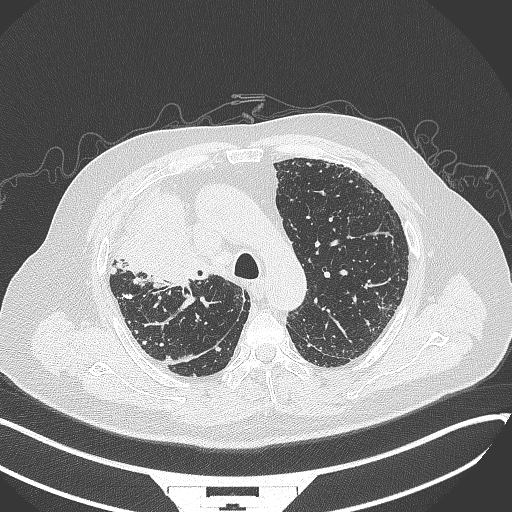
Chest CT, one axial slice. Position 255 of 384 along the scan axis. Lung window (W 1500 / L -600 HU). 1 mm slice thickness. 512 × 512 image matrix, field of view 400 × 400 mm. Patient: male, 69 years. Case-level facts recorded for this patient, not image findings: clinical TNM (as recorded): T4 N3 M1.
Outlined on this slice (rectangle marked by the reading radiologist):
- lung tumour (recorded histology: adenocarcinoma): box from (x=112, y=186) to (x=208, y=291) px